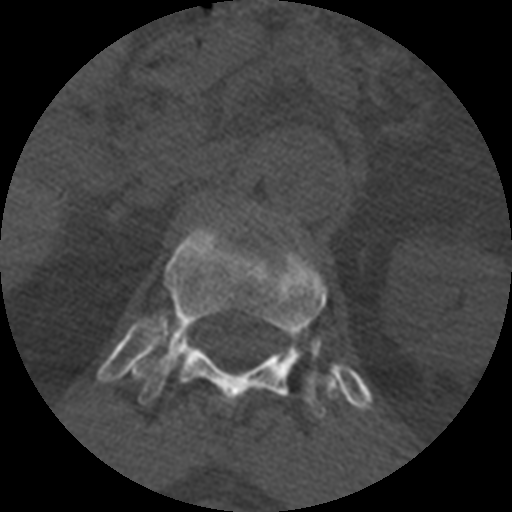
CT including the spine, one axial slice. Slice 384 of 399 in the series (ordered by position). Bone window (W 1800 / L 400 HU). 1.25 mm slice thickness. 512 × 512 image matrix, field of view 160 × 160 mm. Patient age 71 years. From the clinical record (not read from this slice): primary cancer: prostate.
Outlined on this slice (semi-automatically segmented with operator editing):
- T12 vertebra: bounding box (x1, y1, x2, y2) in pixels: (135, 222, 338, 417)